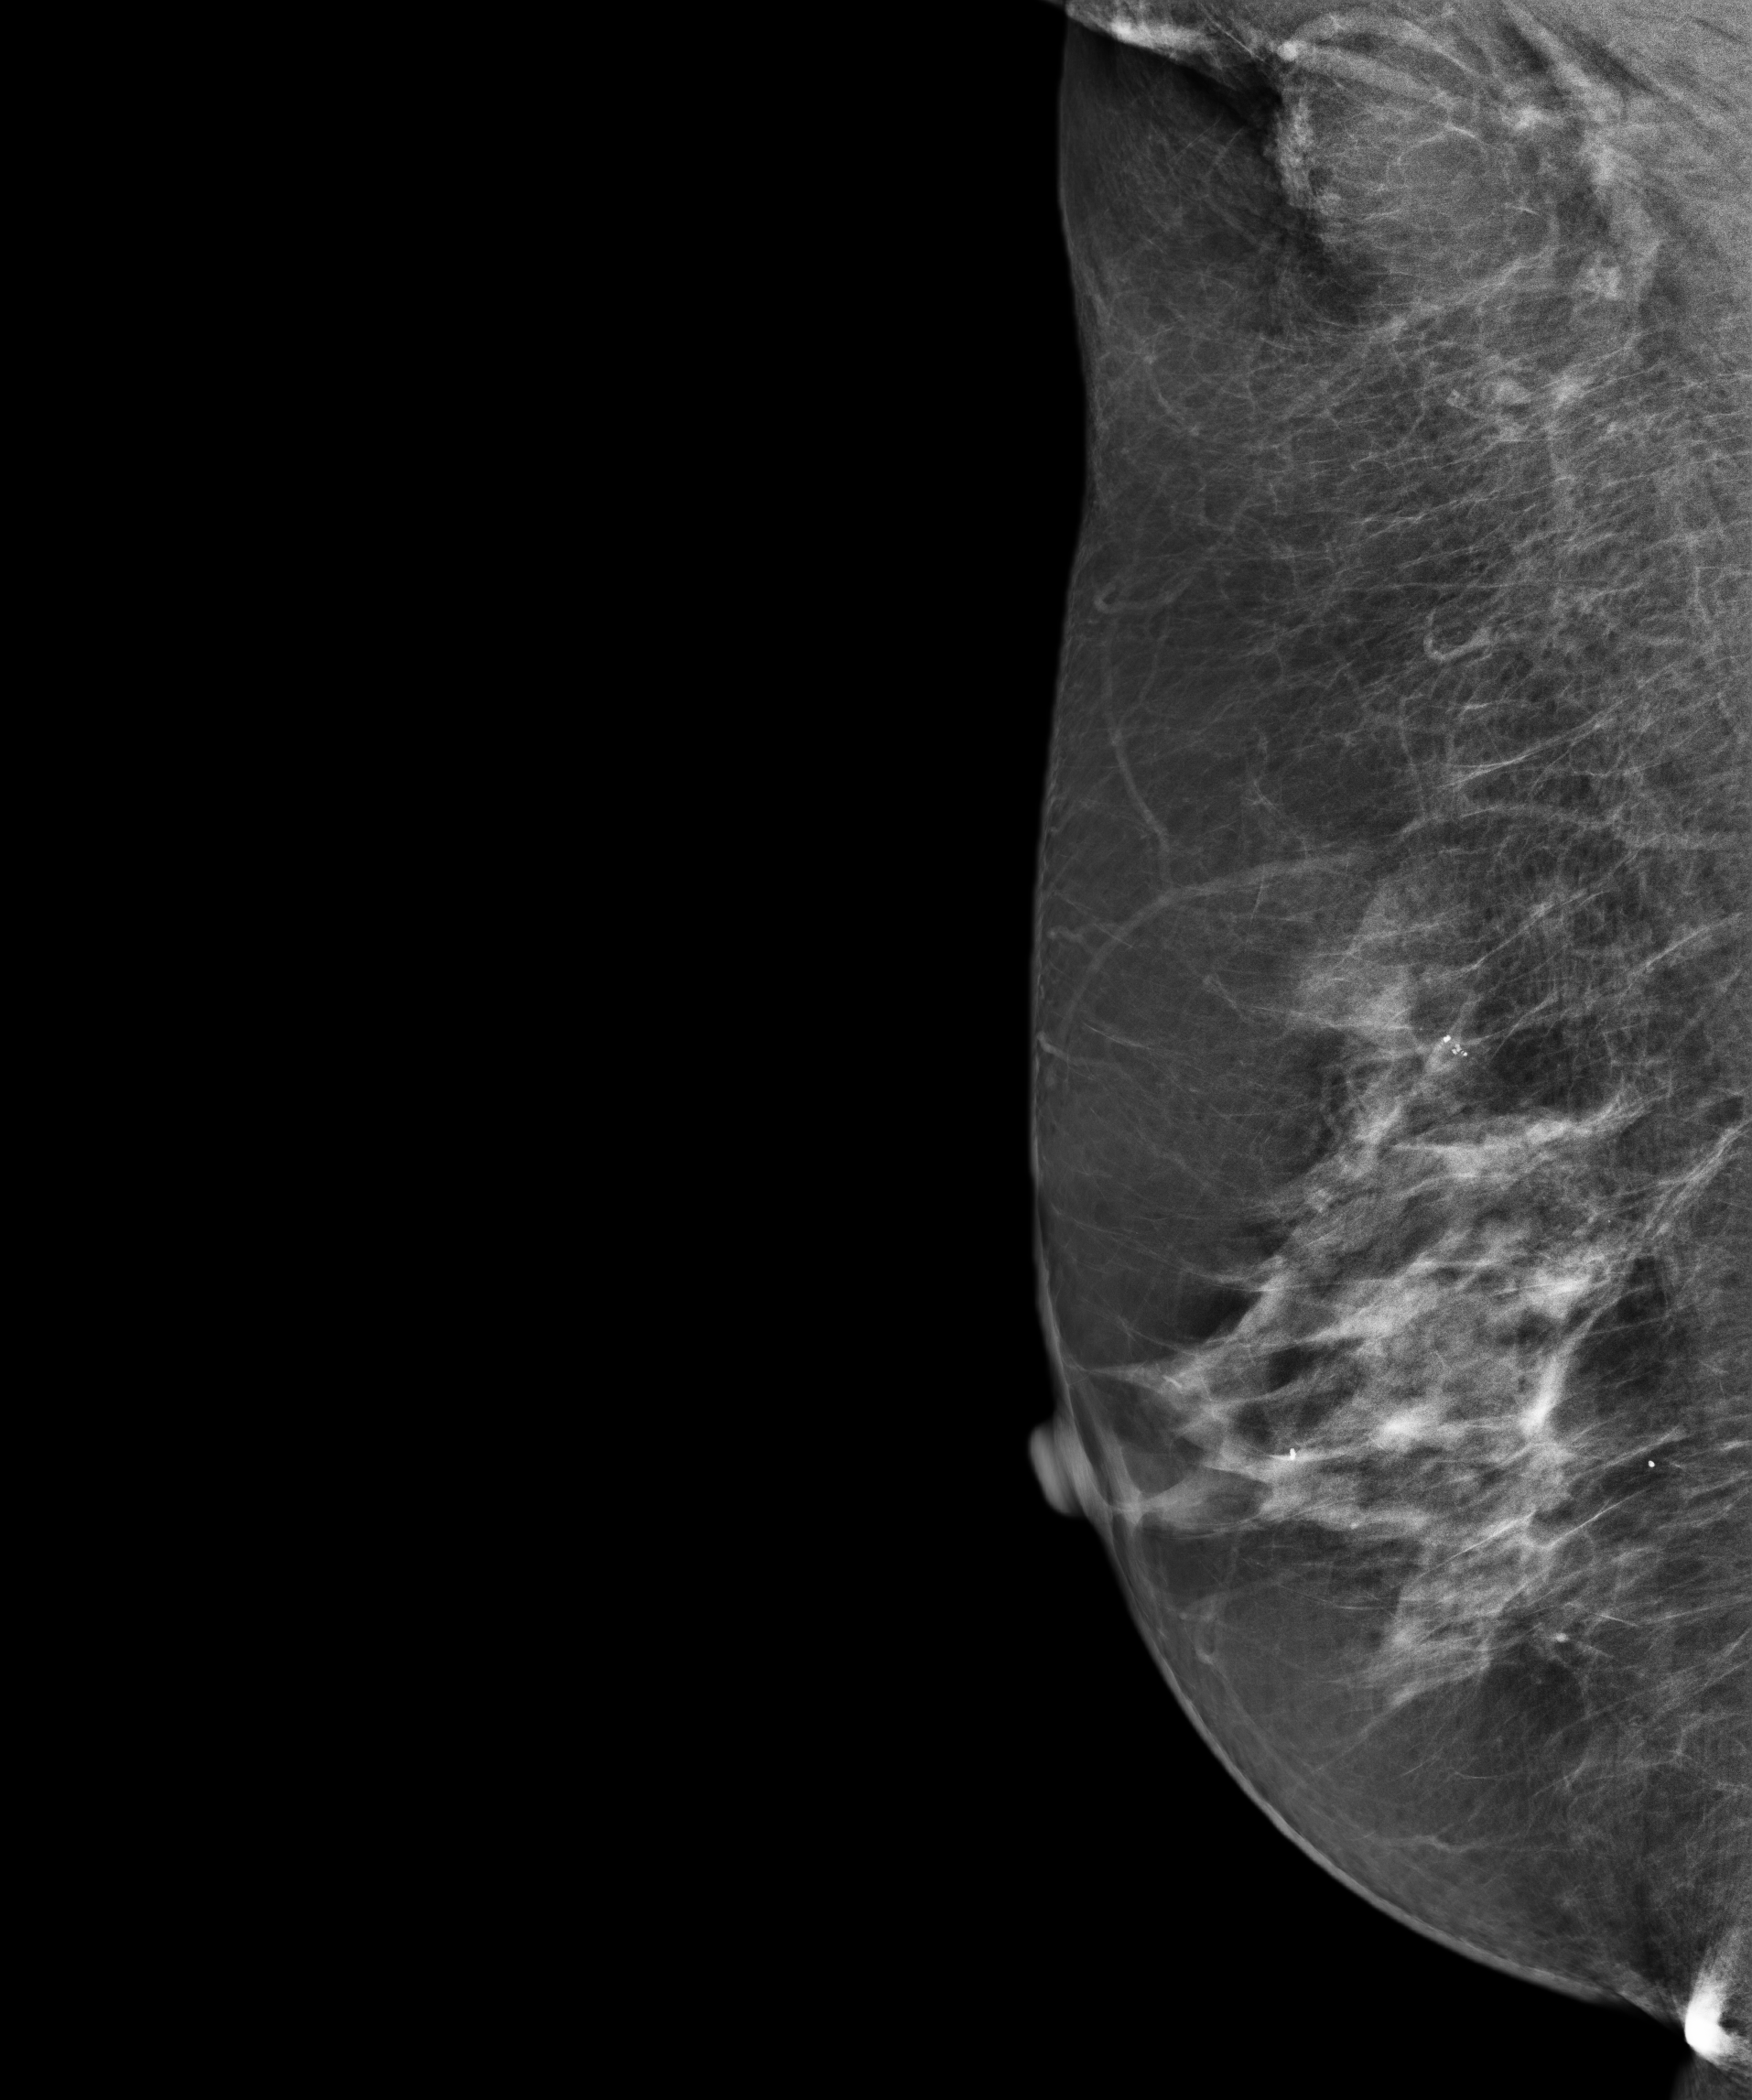
Annual screening mammography examination; system: Senographe Pristina.
Image type: full-field digital mammogram. Breast: right. Projection: MLO view.